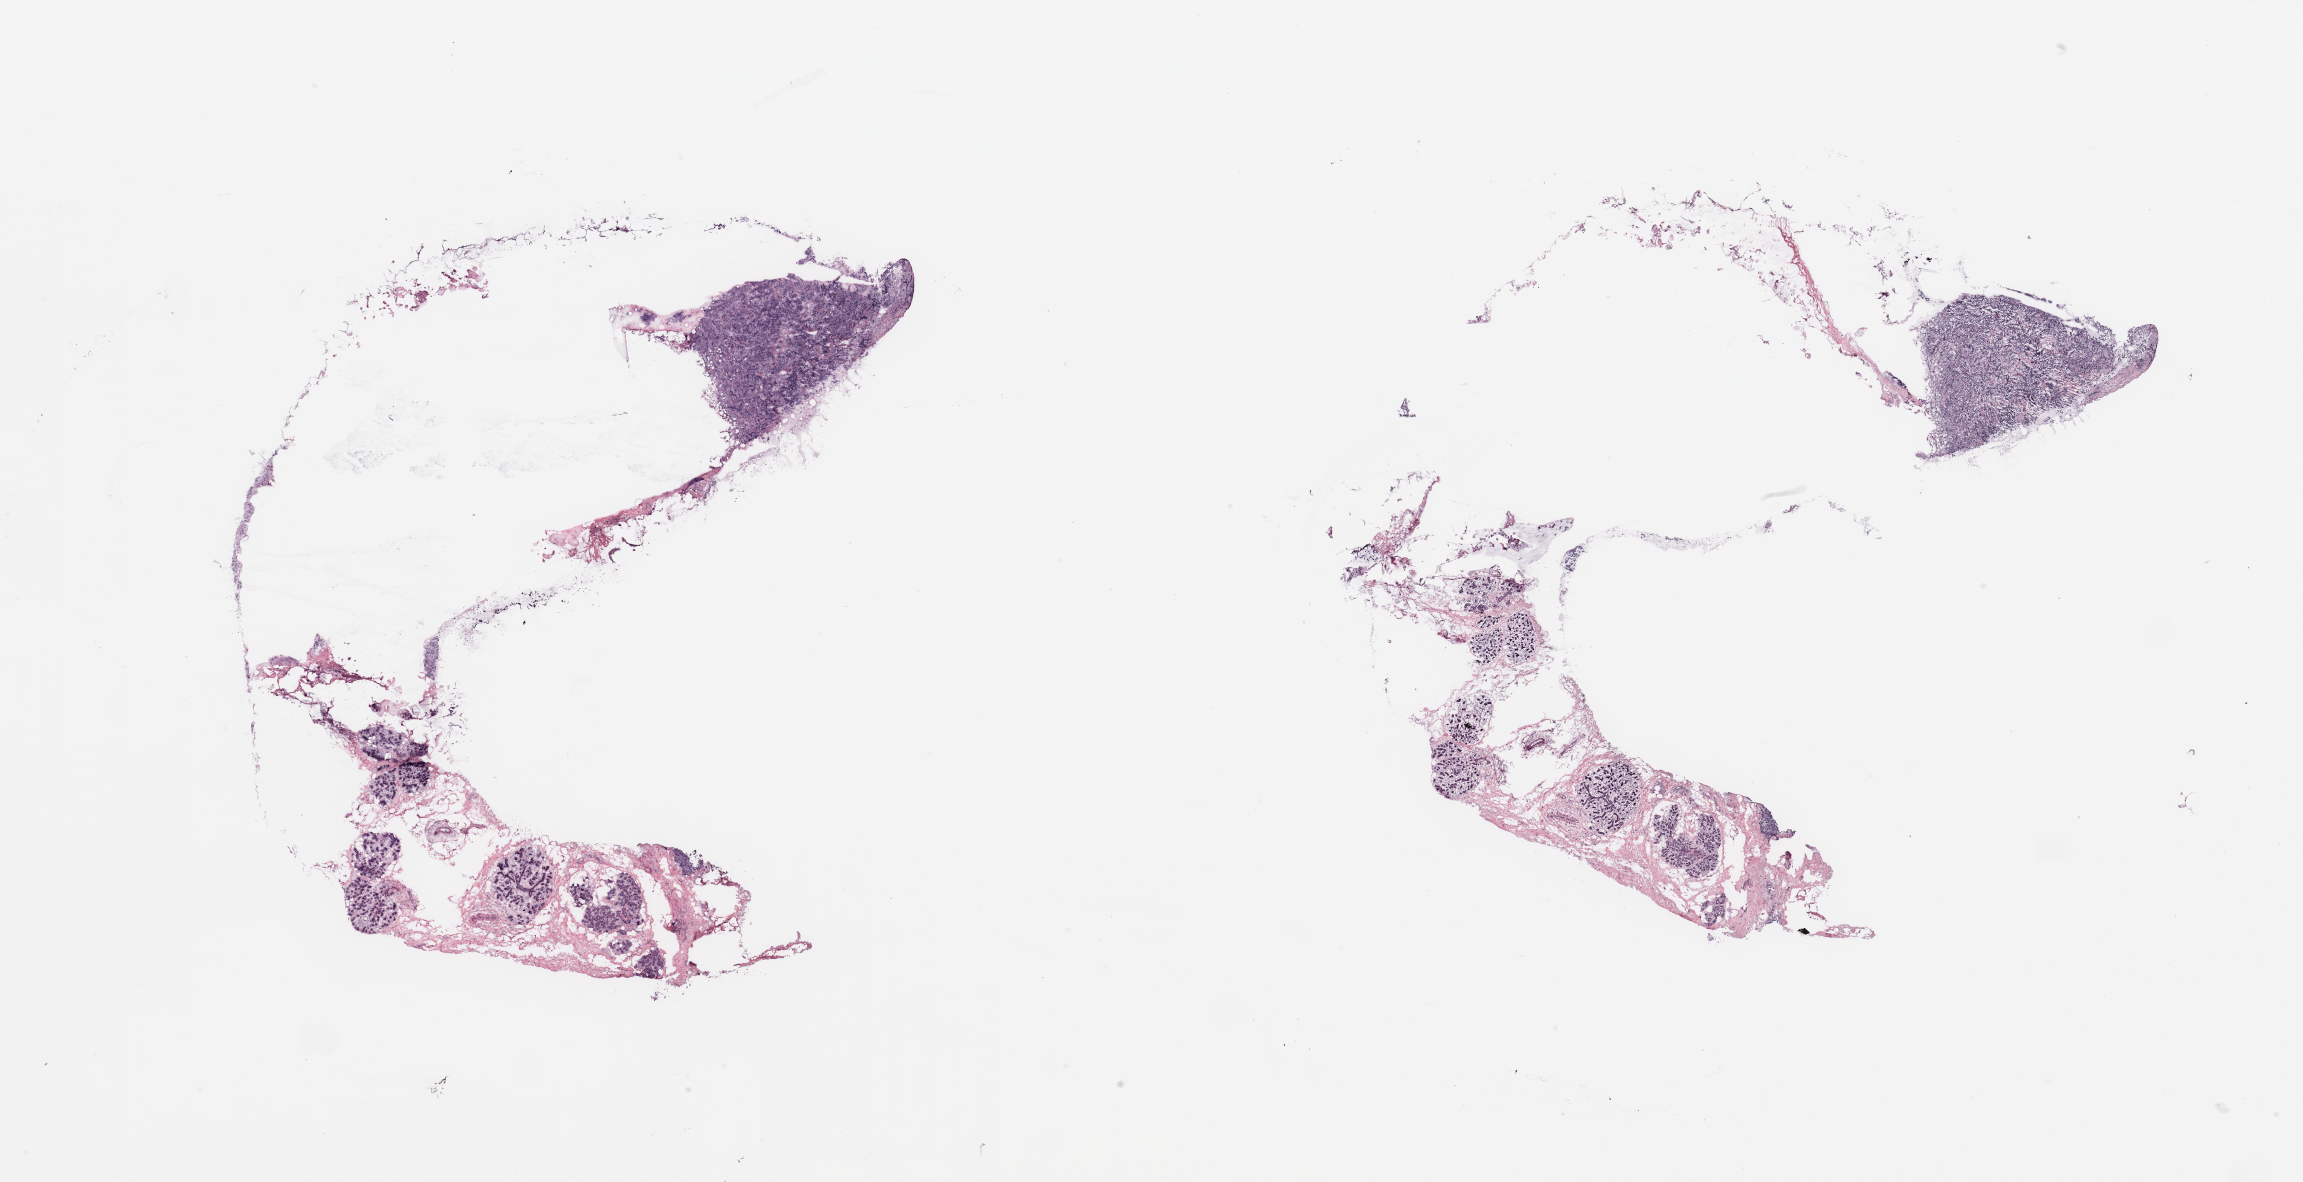
Hematoxylin and eosin (H&E) stained whole-slide image, shown as a low-resolution overview of the whole scanned area (about 36.4 x 18.7 mm, slide scanned at 20x). Patient: female, age 45 years.
• specimen: tumour tissue sample, breast